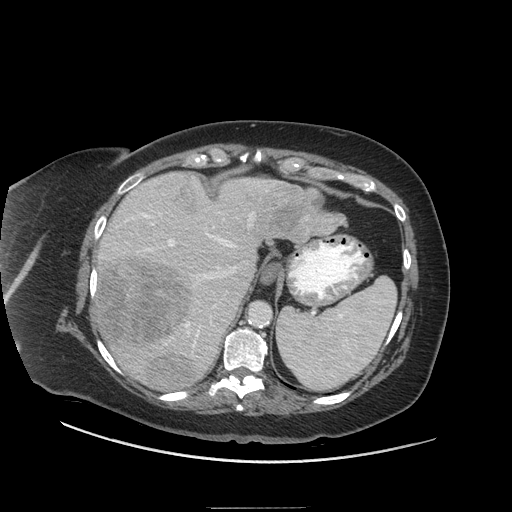
Contrast-enhanced abdominal CT (liver protocol), one axial slice; position 46 of 81 along the scan axis; reconstruction kernel STANDARD; soft-tissue window (W 400 / L 40 HU); 2.5 mm slice thickness; 512 × 512 image matrix. From the clinical record (not read from this slice): diagnosis: hepatocellular carcinoma (patient treated with transarterial chemoembolisation; whether this scan precedes or follows treatment is not stated here); TNM stage (as recorded): Stage-II; Child-Pugh class: A; tumour nodularity: multinodular.
Structures marked on this image (semi-automatically segmented with operator editing):
- liver parenchyma outside the tumour (the mass and vessels are separate outlines, so this box may not span the whole liver): bounding box <92,172,341,384> (left, top, right, bottom; pixels)
- mass: <97,173,346,392>
- liver vessels: <101,180,276,356>